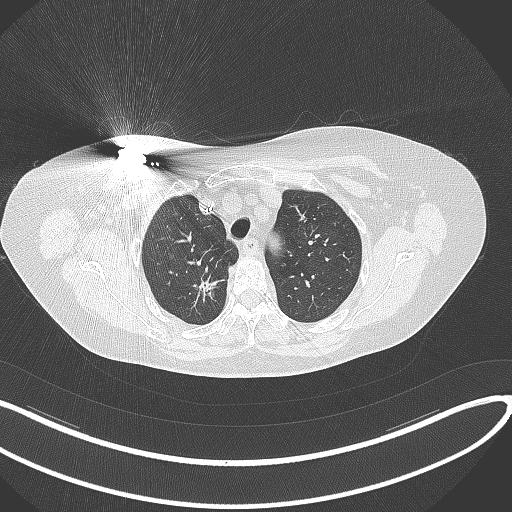
Chest CT, one axial slice. Position 268 of 316 along the scan axis. Reconstruction kernel B70f. Lung window (W 1500 / L -600 HU). 1 mm slice thickness. 512 × 512 image matrix. Female patient, age 72 years. Case-level facts recorded for this patient, not image findings: clinical TNM (as recorded): T1c N0 M0.
Outlined on this slice (rectangle marked by the reading radiologist):
- lung tumour (recorded histology: adenocarcinoma): bounding box (x1, y1, x2, y2) in pixels: (184, 265, 223, 311)